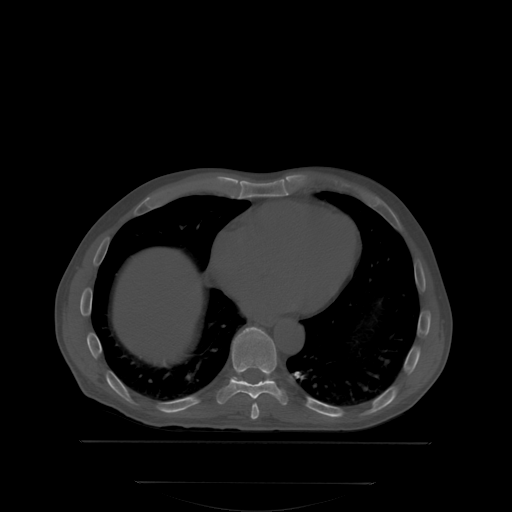
CT including the spine, one axial slice. Slice 204 of 350 in the series (ordered by position). Bone window (W 1800 / L 400 HU). 2.5 mm slice thickness. 512 × 512 image matrix, field of view 500 × 500 mm. Male patient, age 58 years. From the clinical record (not read from this slice): primary cancer: prostate; vertebrae with lytic lesions (as recorded): L1.
Structures marked on this image (semi-automatic segmentation, software-assisted and operator-edited):
- T8 vertebra: bounding box <251,403,260,419> (left, top, right, bottom; pixels)
- T9 vertebra: <218,328,288,403>